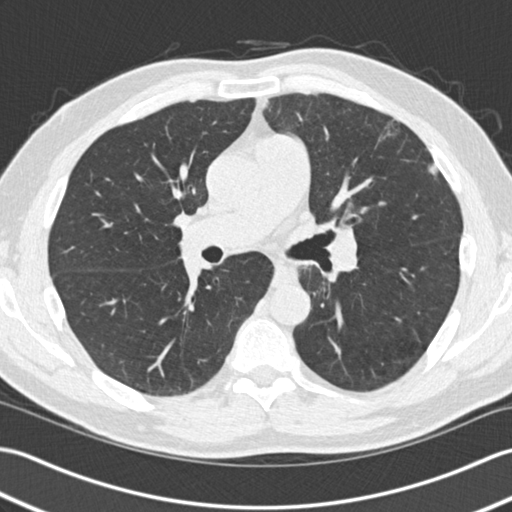
Low-dose screening chest CT, one axial slice. Position 73 of 140 along the scan axis. 120 kVp. Lung window (W 1500 / L -600 HU). 2 mm slice thickness. 512 × 512 image matrix.
Annotated regions visible in this slice (expert manual segmentation):
- lesion 1 (tumor, upper lobe of left lung): bounding box <429,163,439,175> (left, top, right, bottom; pixels)